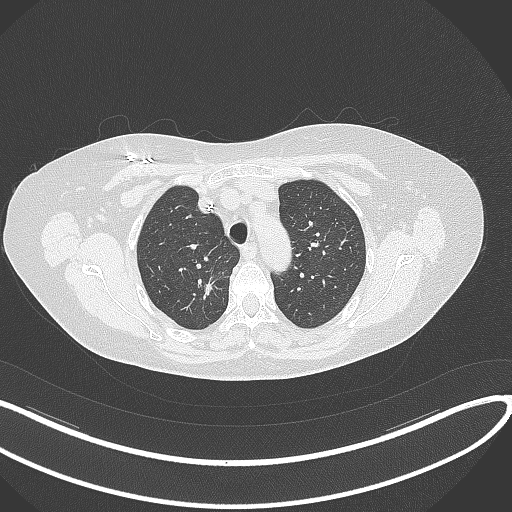
Chest CT, one axial slice. Slice 259 of 316 in the series (ordered by position). Reconstruction kernel B70f. 120 kVp. Lung window (W 1500 / L -600 HU). 512 × 512 image matrix, field of view 400 × 400 mm. Female patient, age 72 years. Case-level facts recorded for this patient, not image findings: clinical TNM (as recorded): T1c N0 M0.
Outlined on this slice (rectangle marked by the reading radiologist):
- lung tumour (recorded histology: adenocarcinoma): bounding box <194,275,223,308> (left, top, right, bottom; pixels)